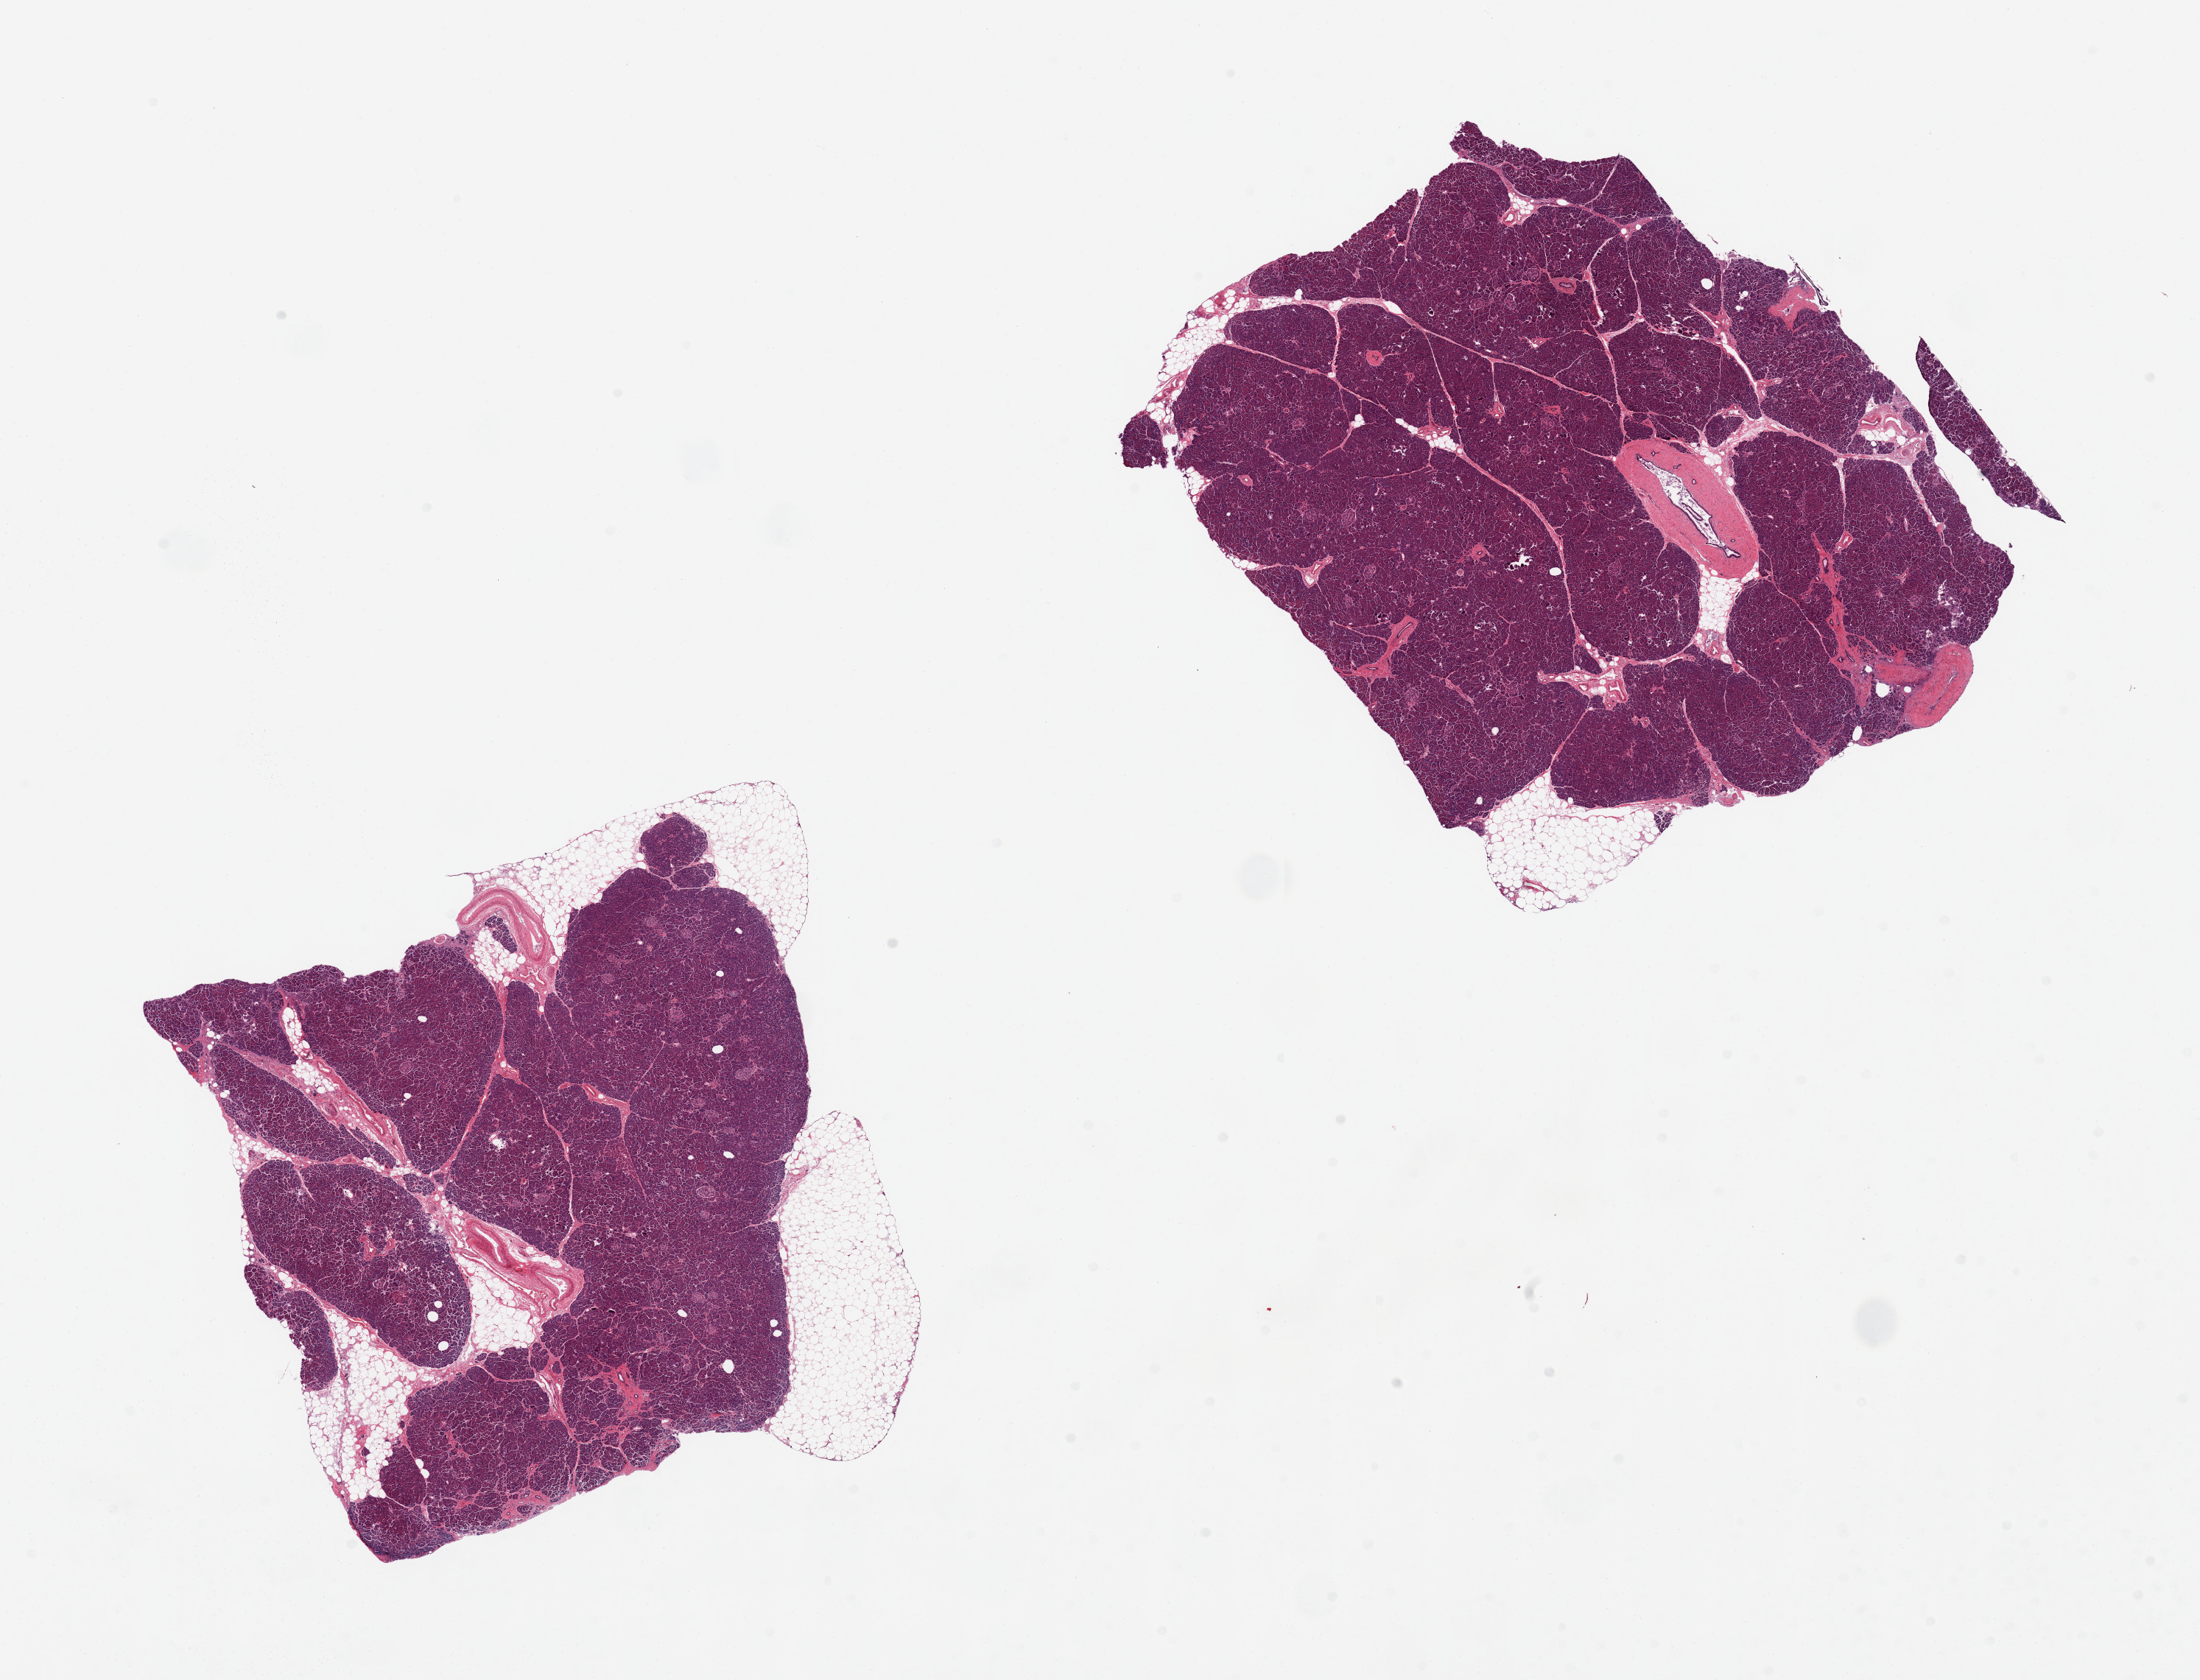
Whole-slide image, hematoxylin and eosin (H&E) stain — shown as a low-resolution overview of the whole scanned area (about 23.6 x 18.0 mm, slide scanned at 20x). PAXgene-fixed, paraffin-embedded tissue. Section of pancreas (target tissue). Tissue donor sample. Donor: male.
Reviewer comment on this tissue sample: 2 pieces; plentiful islets of Langerhans; 10% and >5% of external far; 1 piece contains 5% internal fat.